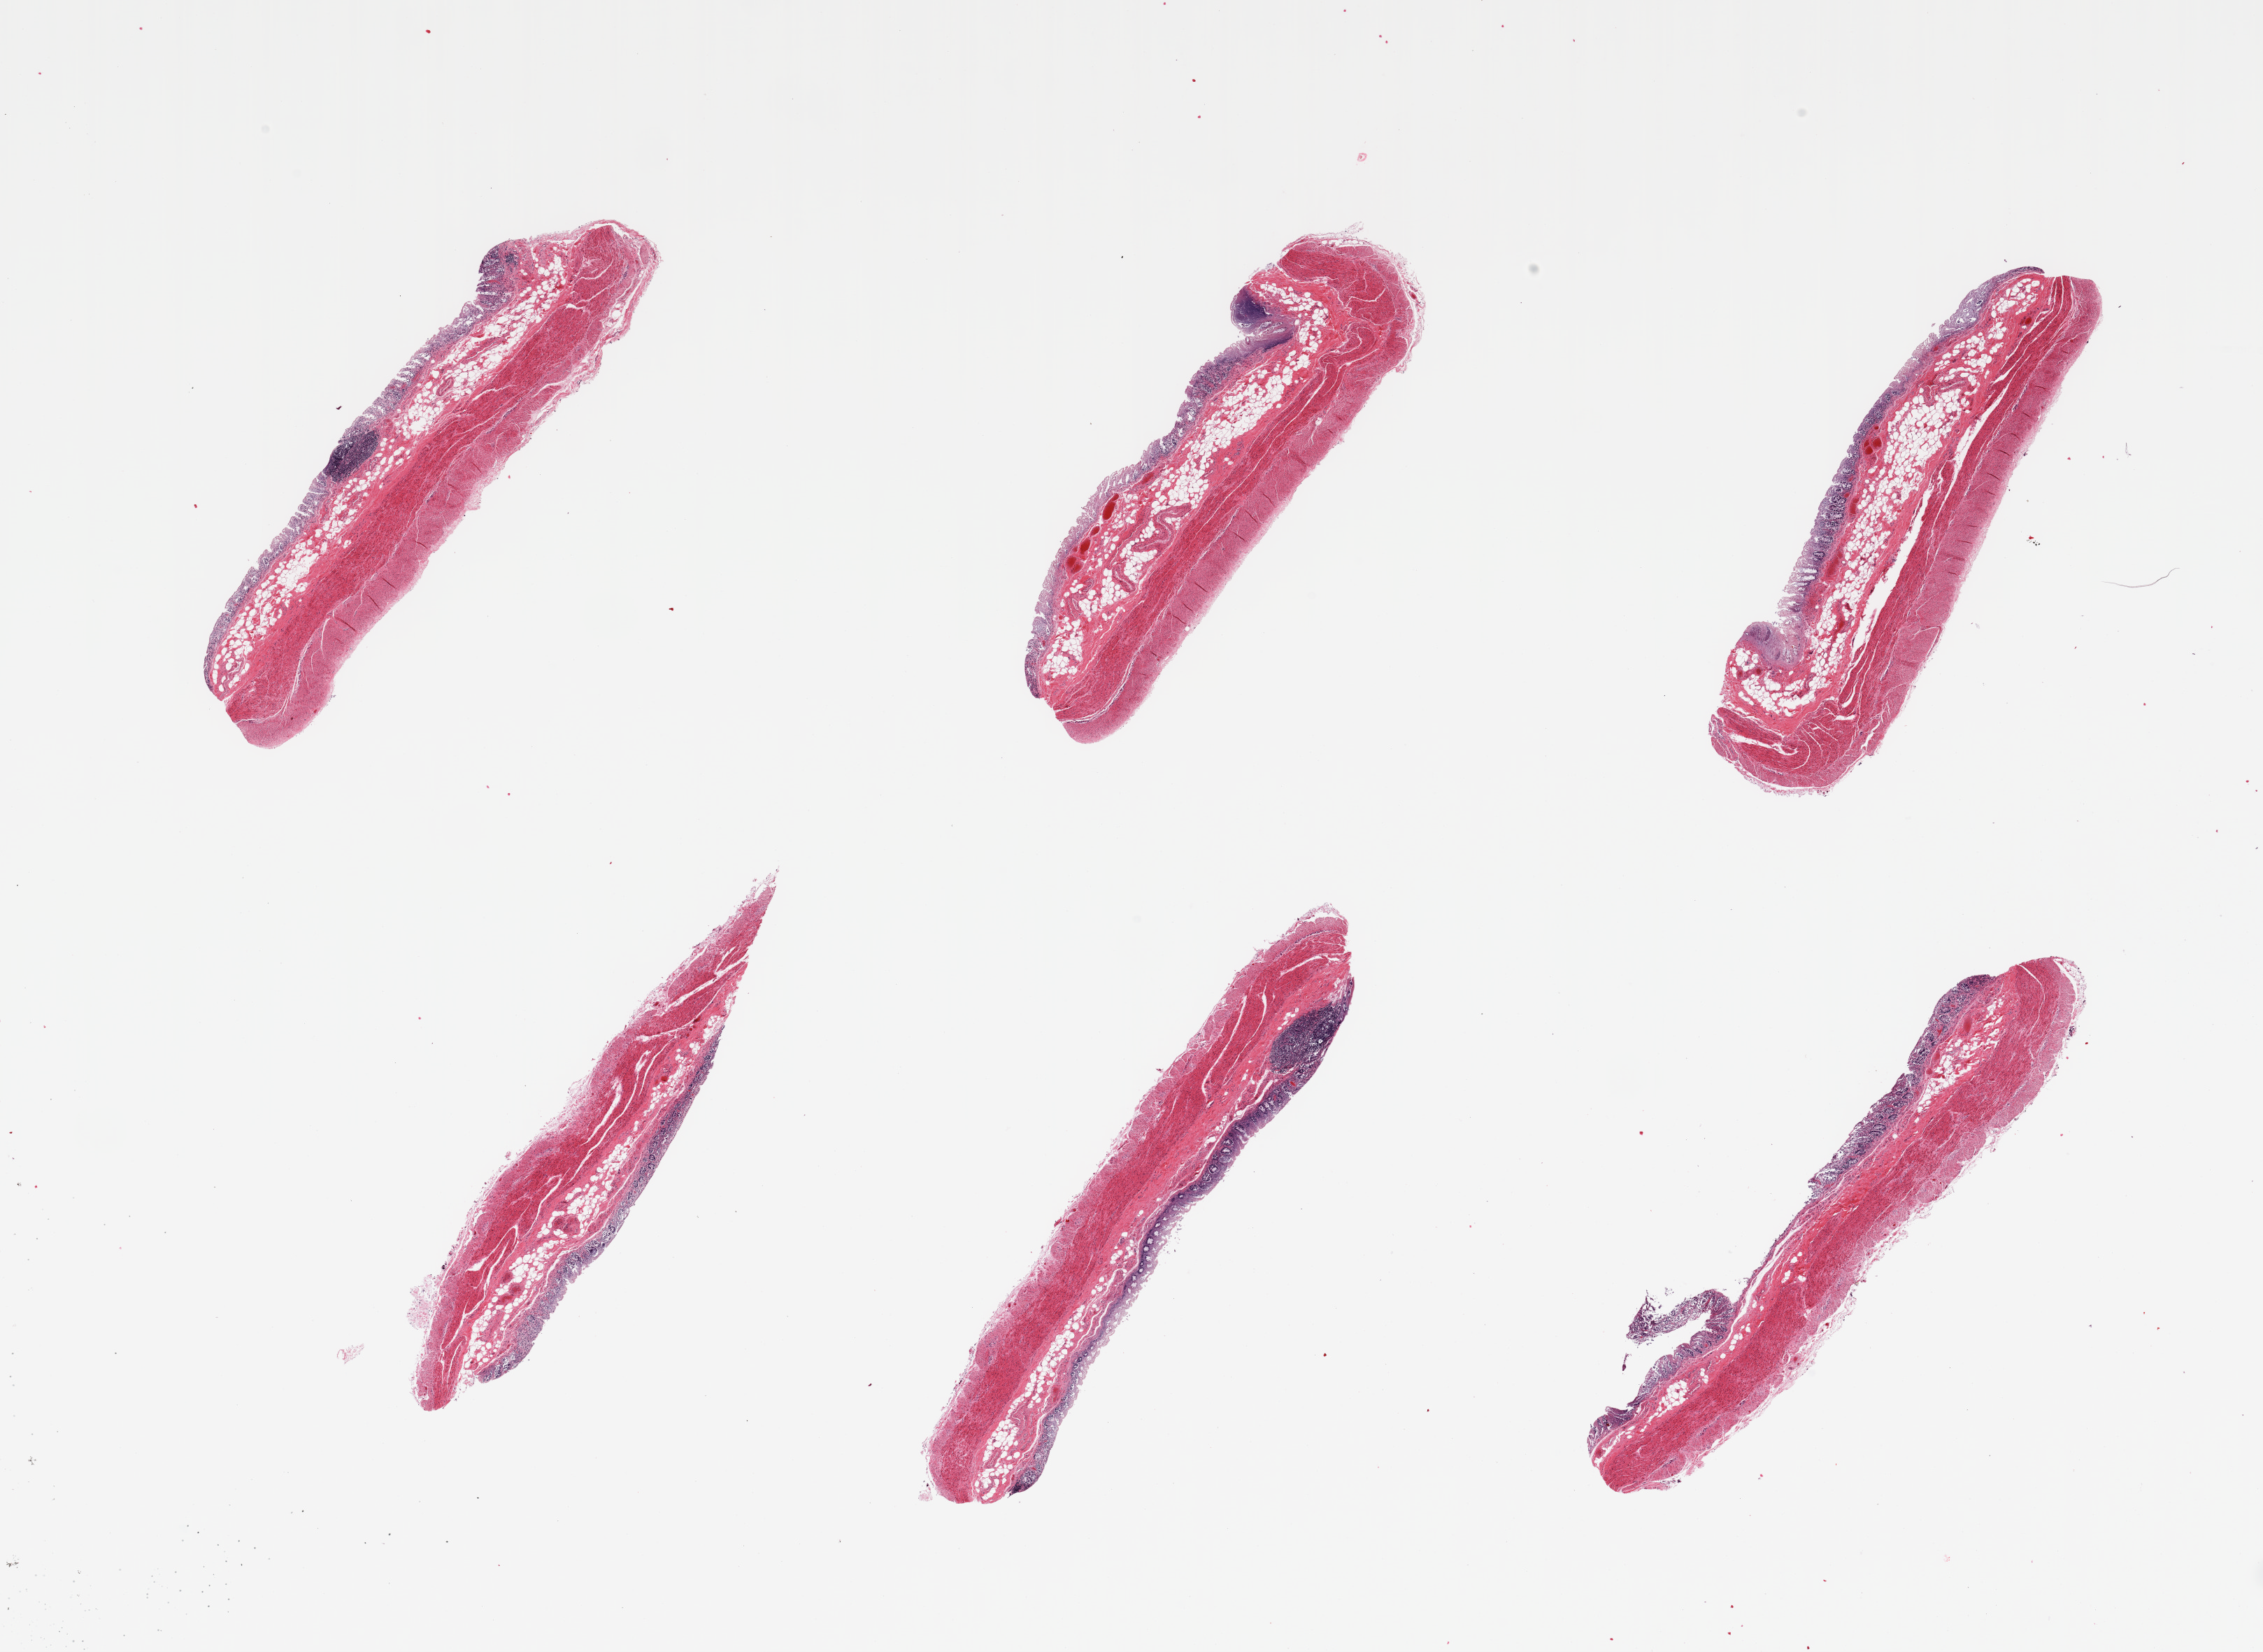
Haematoxylin and eosin whole-slide image — low-resolution overview of the scanned area, about 25.6 x 18.7 mm. PAXgene-fixed paraffin-embedded (PFPE) section. Sampled site (target tissue): transverse colon. Donor tissue sample.
• pathologist's review note for this sample: 6 pieces, mucosa up to ~0.2mm, total glandular autolysis/sloughing